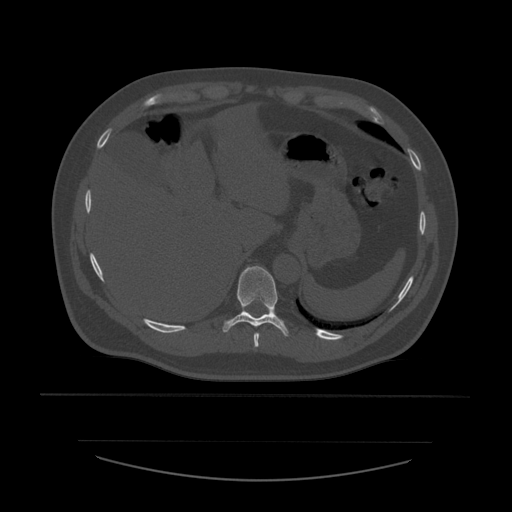
CT including the spine, one axial slice. Position 298 of 532 along the scan axis. Reconstruction kernel STANDARD. 120 kVp. Bone window (W 1800 / L 400 HU). 1.25 mm slice thickness. 512 × 512 image matrix, field of view 441 × 441 mm. Patient age 44 years. From the clinical record (not read from this slice): primary cancer: soft tissue sarcoma.
Structures marked on this image (semi-automatically segmented with operator editing):
- T10 vertebra: bounding box <223,266,289,337> (left, top, right, bottom; pixels)
- T9 vertebra: <254,333,260,348>